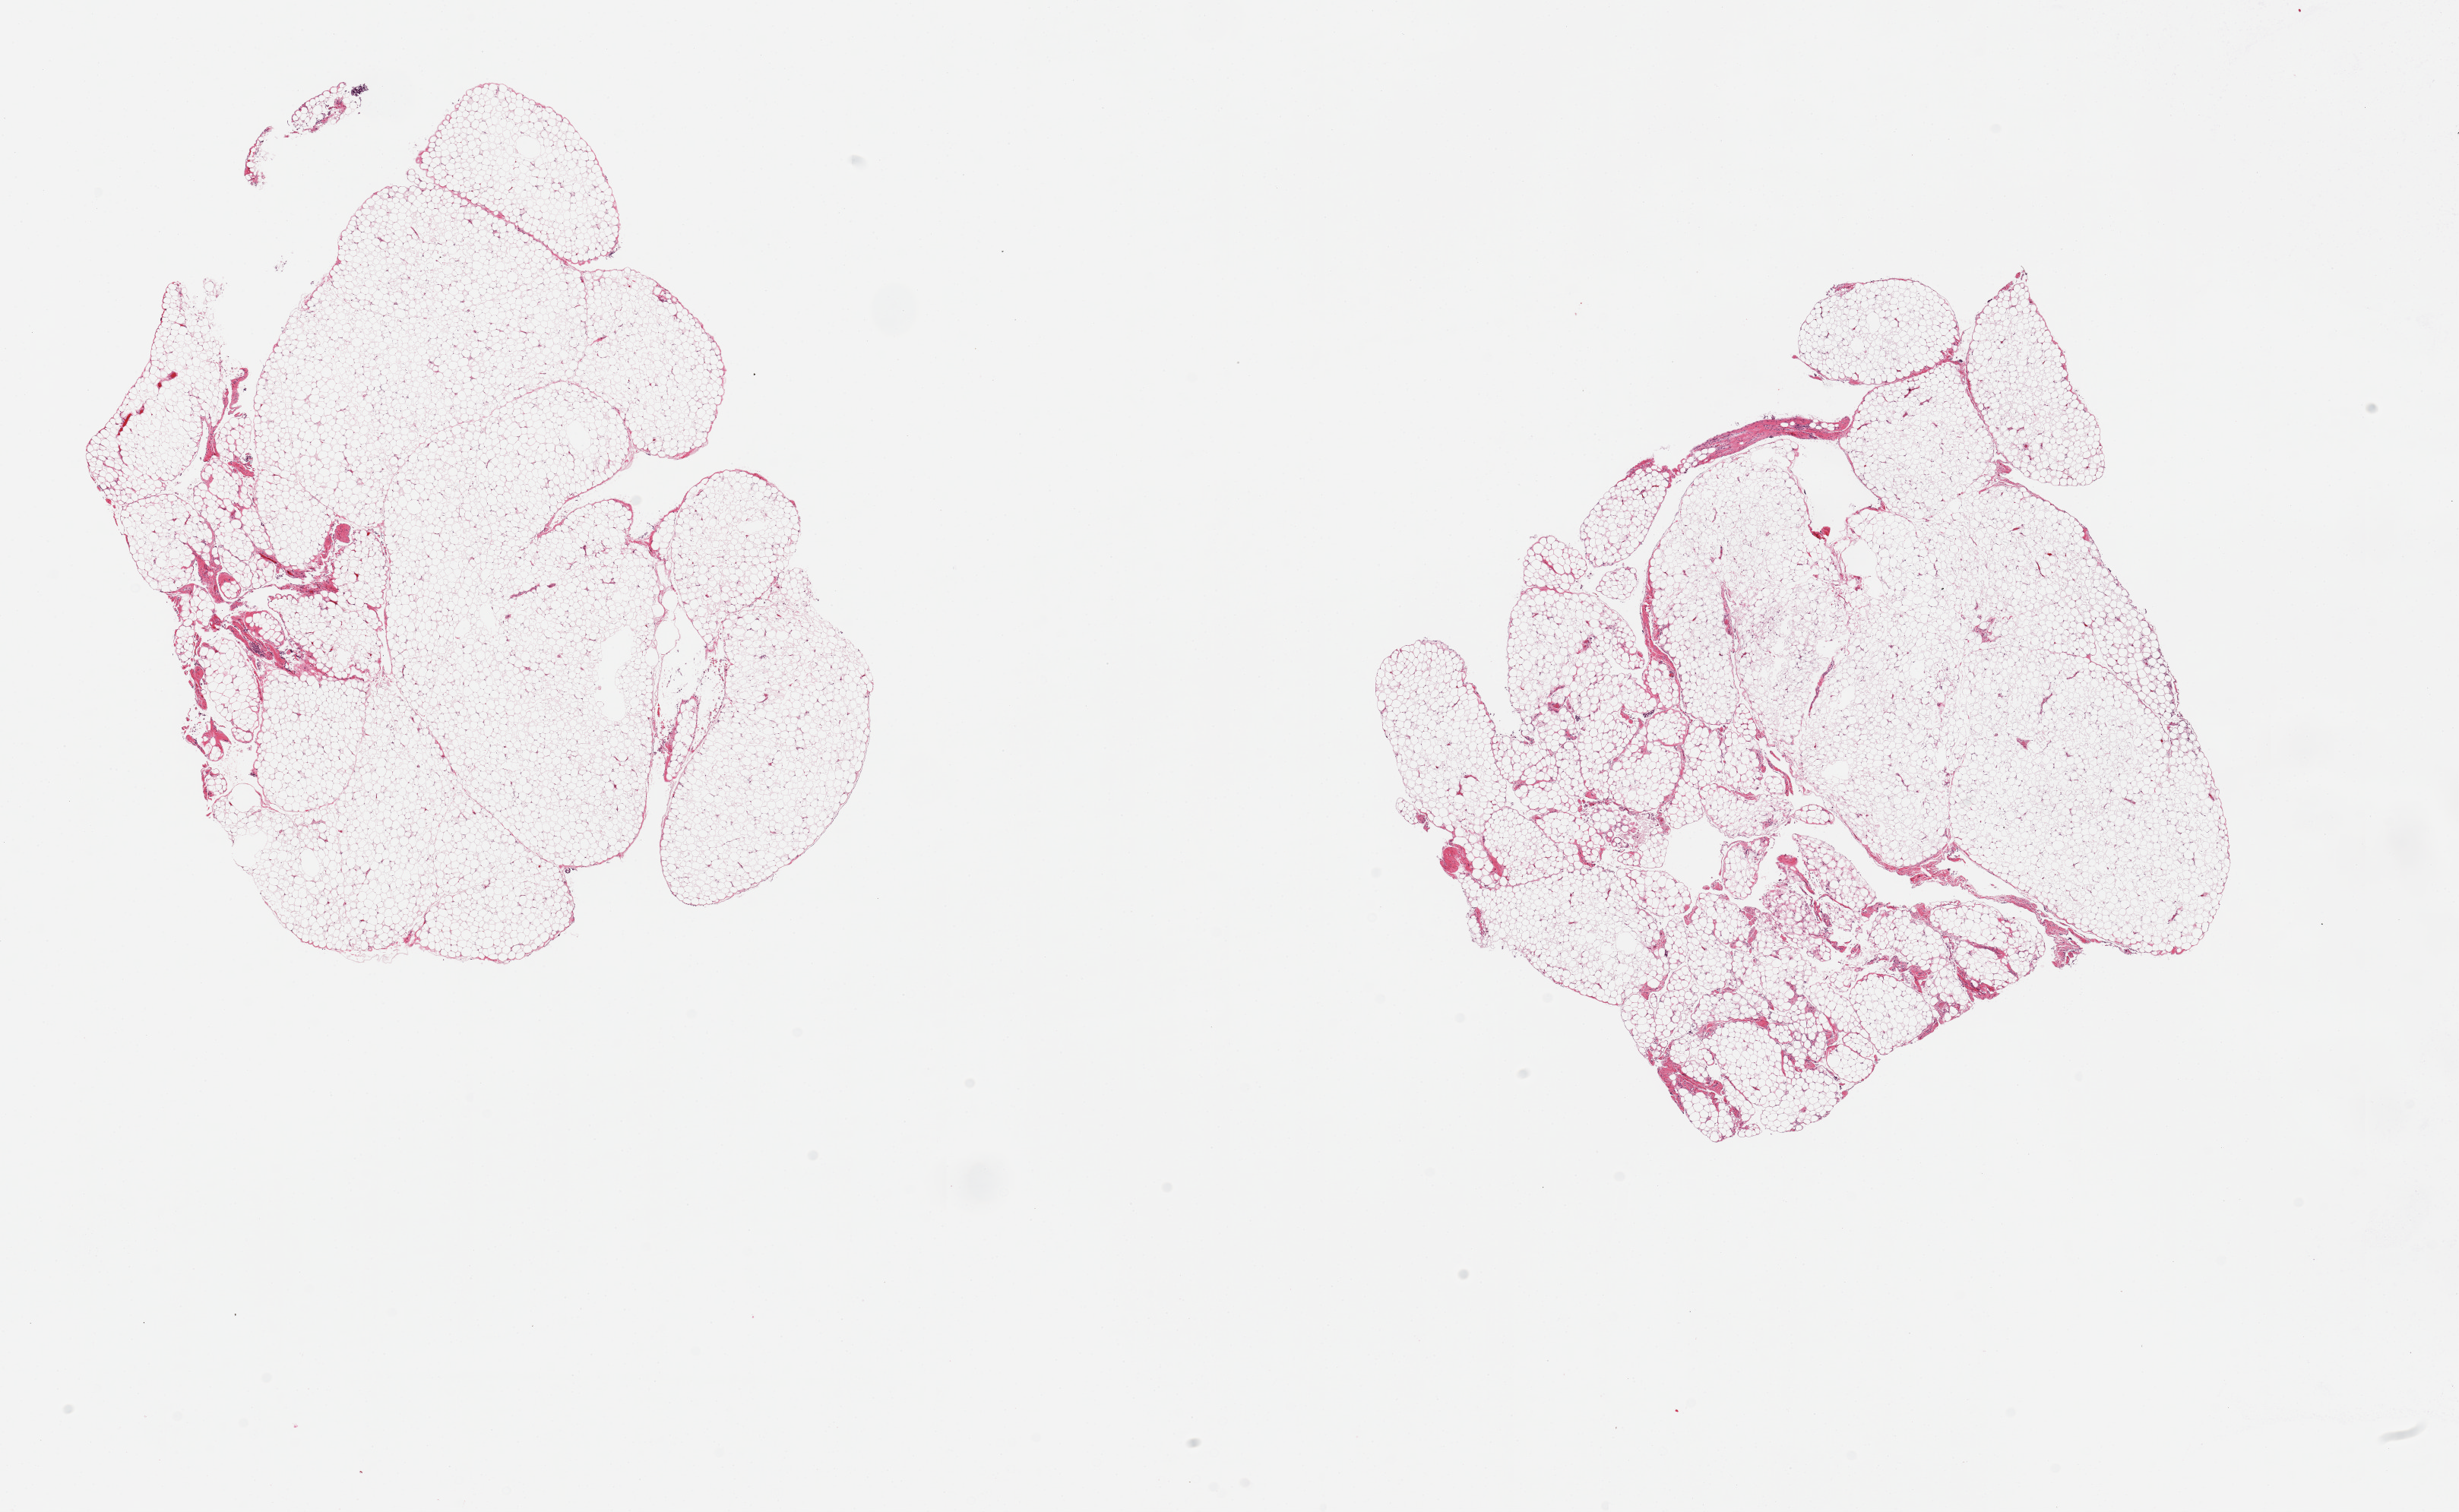
Whole-slide image, hematoxylin and eosin (H&E) stain — low-resolution overview of the scanned area, about 25.6 x 15.7 mm; PAXgene-fixed paraffin-embedded (PFPE) section; sampled site (target tissue): omentum; donor tissue sample. Donor sex: male.
Review note (as recorded): 2 pieces, minimal vascular/mesothelial tissue.